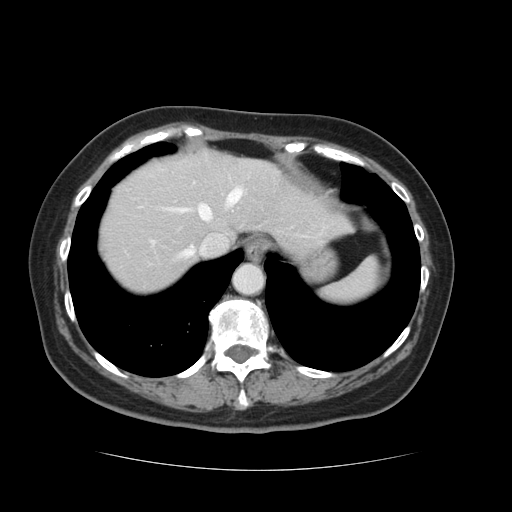
Contrast-enhanced abdominal CT, one axial slice; slice 107 of 128 in the series (ordered by position); 120 kVp; intravenous contrast given; soft-tissue window (W 400 / L 40 HU); 2.5 mm slice thickness; 512 × 512 image matrix. Female patient, age 67 years. From the clinical record (not read from this slice): diagnosis: colorectal cancer liver metastases, imaged before liver resection; multiple liver metastases: yes; largest metastasis: 3 cm; disease in both lobes: yes.
Annotated regions visible in this slice (outlined manually by an expert reader):
- hepatic veins: bounding box [x1, y1, x2, y2] px = [169, 187, 244, 259]
- liver: [97, 150, 345, 296]
- planned liver remnant (the part of the liver to remain after resection): [98, 158, 347, 295]
- portal vein (with intrahepatic branches): [193, 182, 195, 184]